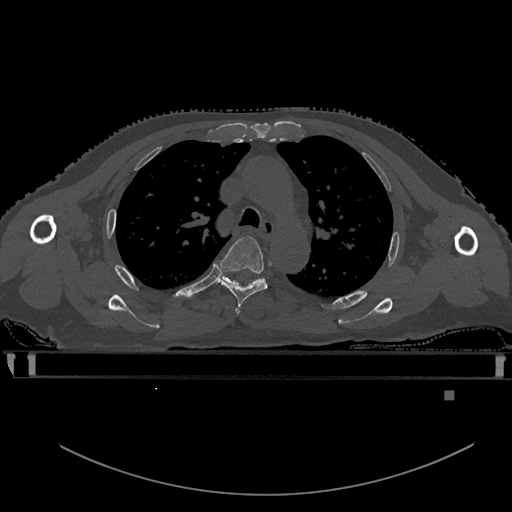
CT including the spine, one axial slice; slice 397 of 969 in the series (ordered by position); bone window (W 1800 / L 400 HU); 0.5 mm slice thickness; 512 × 512 image matrix, field of view 456 × 456 mm. Male patient, age 82 years. From the clinical record (not read from this slice): primary cancer: prostate.
Structures marked on this image (semi-automatically segmented with operator editing):
- T3 vertebra: bounding box <236,308,240,314> (left, top, right, bottom; pixels)
- T4 vertebra: <218,236,268,309>
- T5 vertebra: <218,272,263,285>